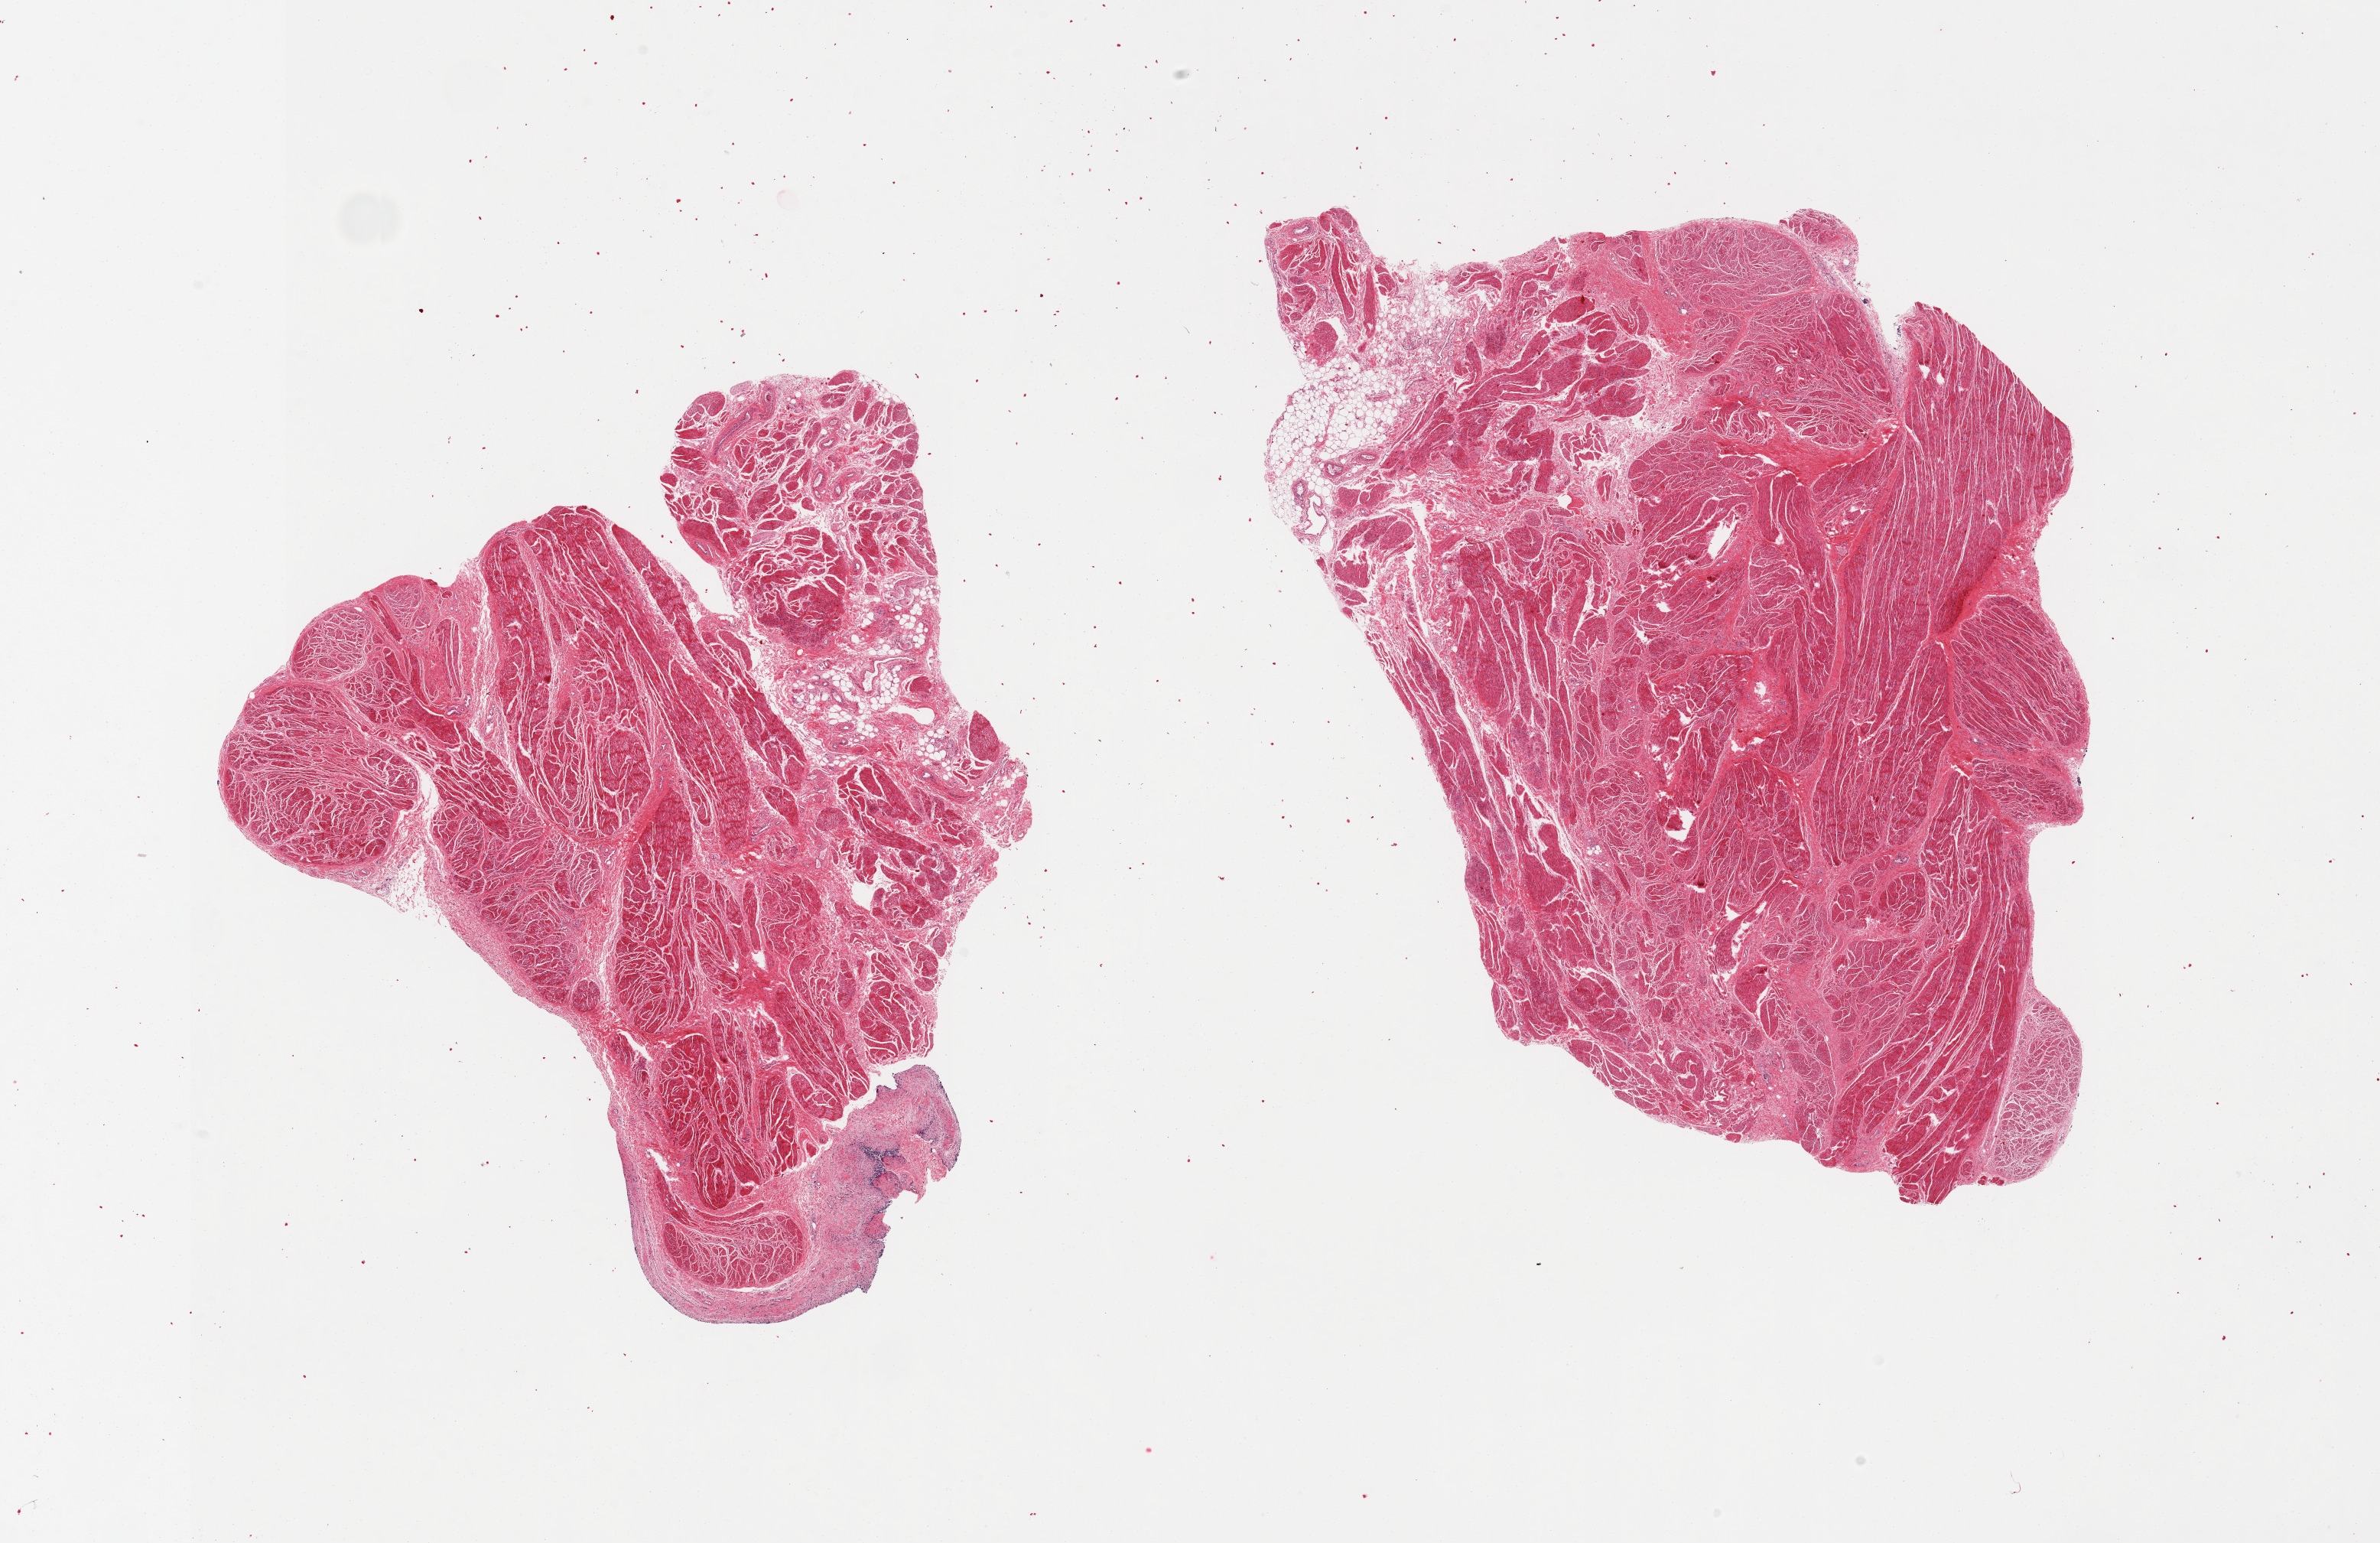
Digitized hematoxylin and eosin (H&E)-stained section, brightfield — low-resolution overview of the scanned area, about 24.6 x 16.0 mm; PAXgene-fixed, paraffin-embedded tissue; sampled site (target tissue): prostate; donor tissue sample. Donor sex: male.
Pathologist's review note for this sample: 2 pieces; no prostate; appears to be bladder wall.